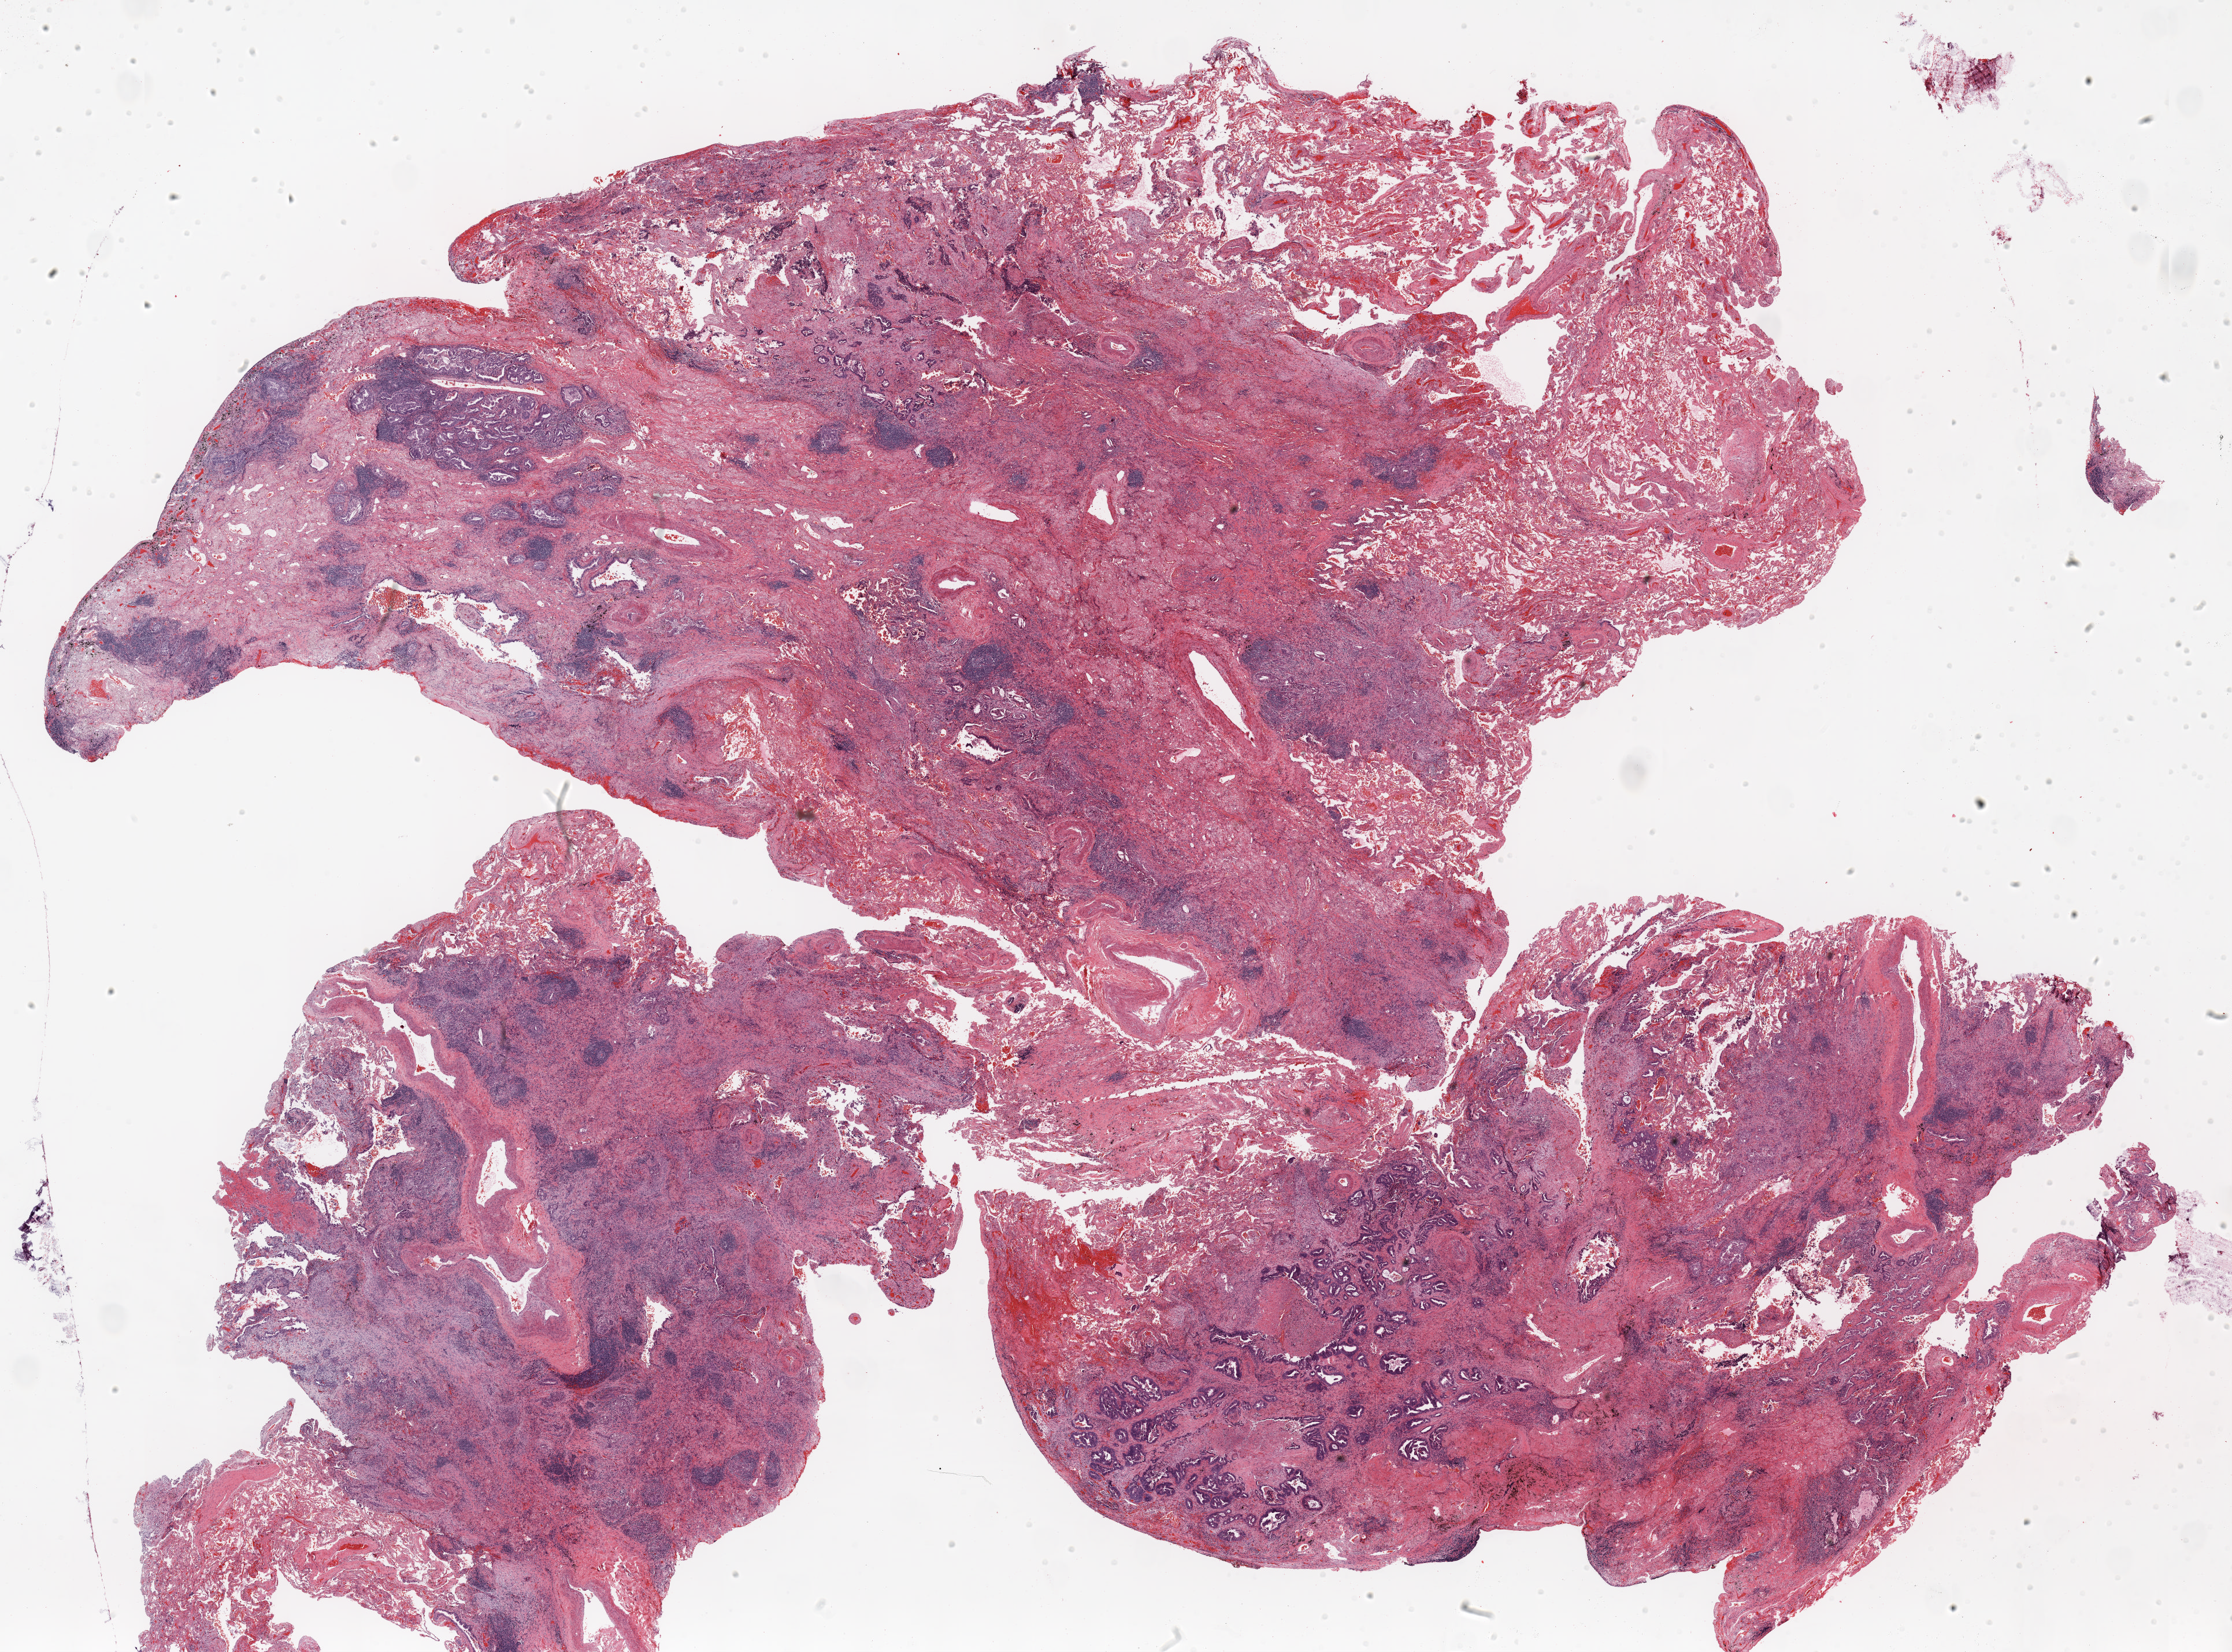
Whole-slide histology image, H&E, whole scanned area (about 31.0 x 23.0 mm) shown as a low-resolution overview. Formalin-fixed paraffin-embedded (FFPE) section. Lung. Male, age 73 at enrolment. Former smoker at enrolment. Grade: poorly differentiated (G3).
Participant's lung-cancer diagnosis: Adenocarcinoma, NOS. Primary tumour location (clinical record): right upper lobe. Stage (AJCC 6th edition): IA. Tumour size (pathology): 30 mm.